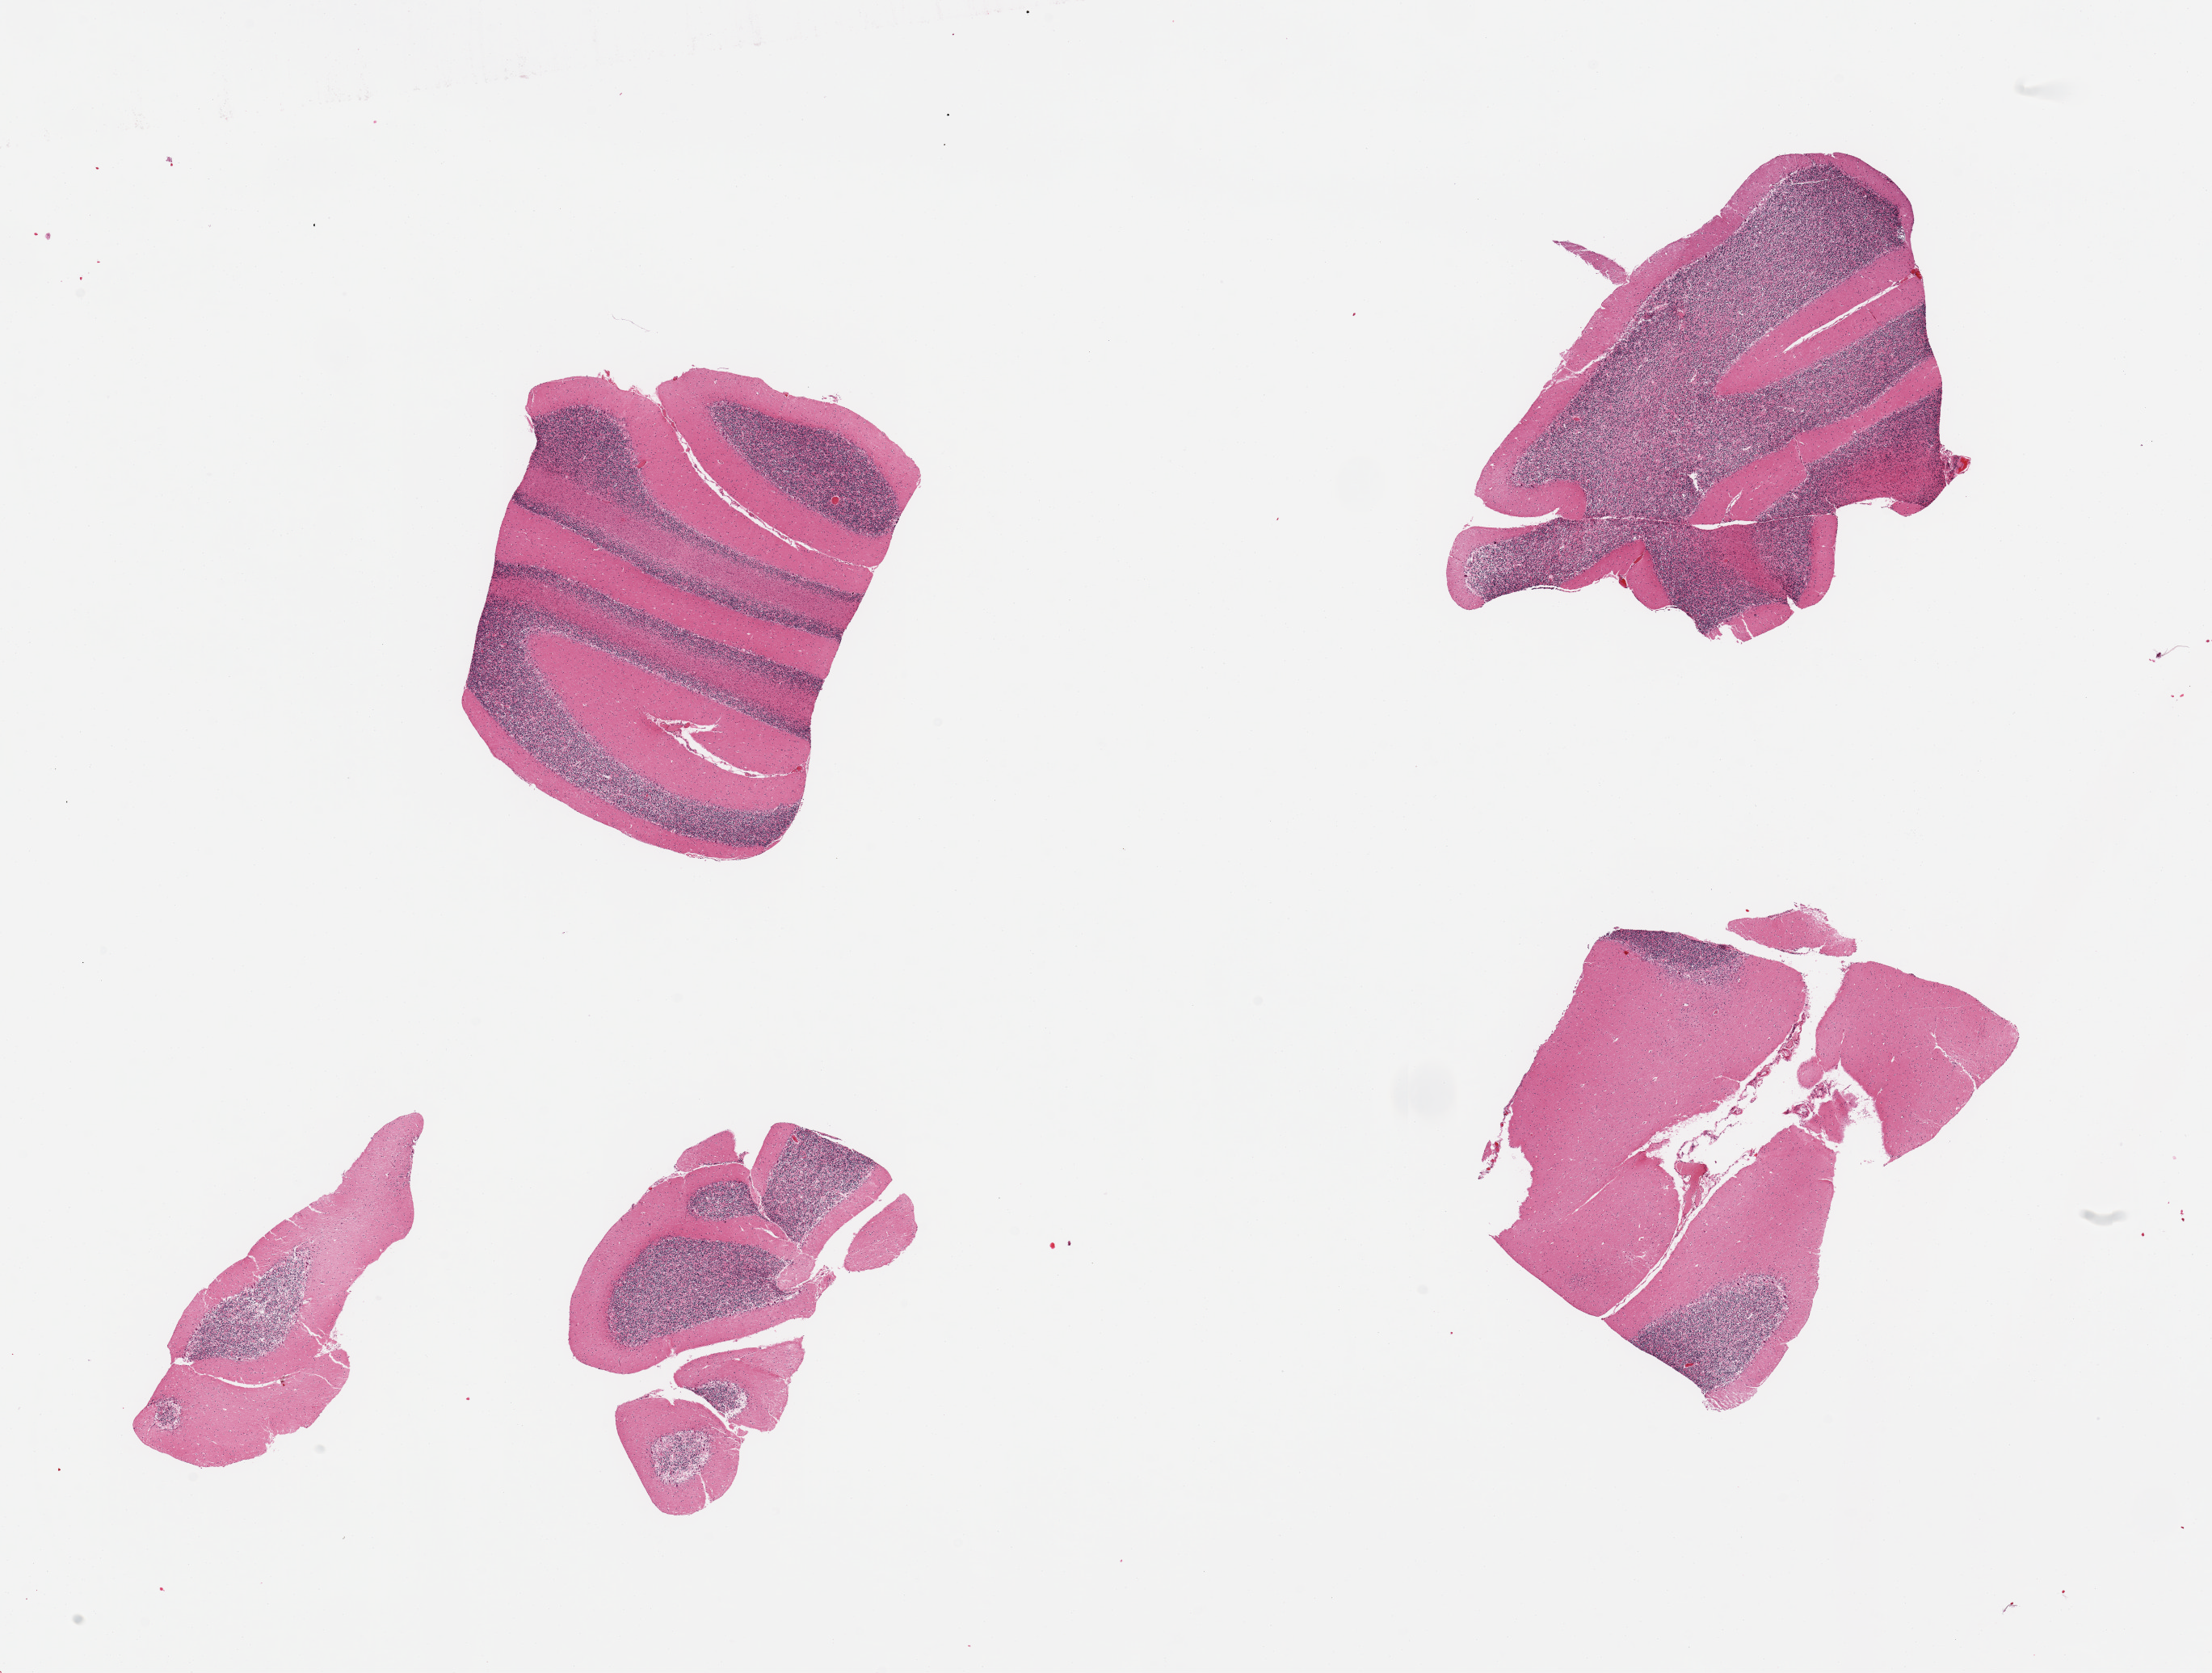
Digitized H&E-stained section, brightfield — low-resolution overview of the scanned area, about 21.7 x 16.4 mm (slide scanned at 20x), PAXgene-fixed paraffin-embedded (PFPE) section, sampled site (target tissue): cerebellum, donor tissue sample. Male donor.
• reviewer comment on this tissue sample: 4 fragmented pieces